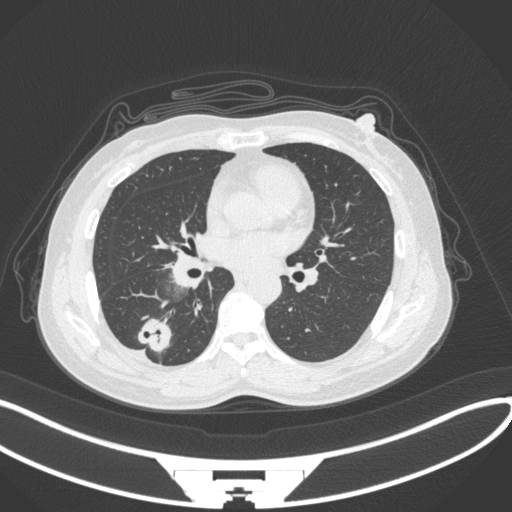
Chest CT, one axial slice. Slice 147 of 352 in the series (ordered by position). Reconstruction kernel B31f. Lung window (W 1500 / L -600 HU). 512 × 512 image matrix. Patient: female, 55 years. From the clinical record (not read from this slice): clinical TNM (as recorded): T1c N1 M0.
Outlined on this slice (bounding box drawn by a radiologist):
- lung tumour (recorded histology: adenocarcinoma): bounding box (x1, y1, x2, y2) in pixels: (135, 315, 180, 356)